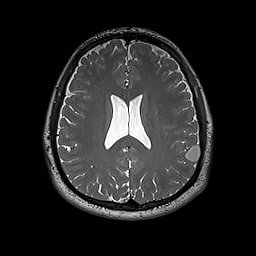
Brain MRI from a brain-tumour surgery series, one axial slice; slice 80 of 192 in the series (ordered by position); 1 mm slice thickness; 256 × 256 image matrix. From the clinical record (not read from this slice): histopathology: Dysembryoplastic neuroepithelial tumor; WHO grade: 1; IDH mutation: no; tumour location: Left Inferior Parietal.
Outlined on this slice (outlined manually by an expert reader):
- tumour: bounding box <185,146,201,162> (left, top, right, bottom; pixels)